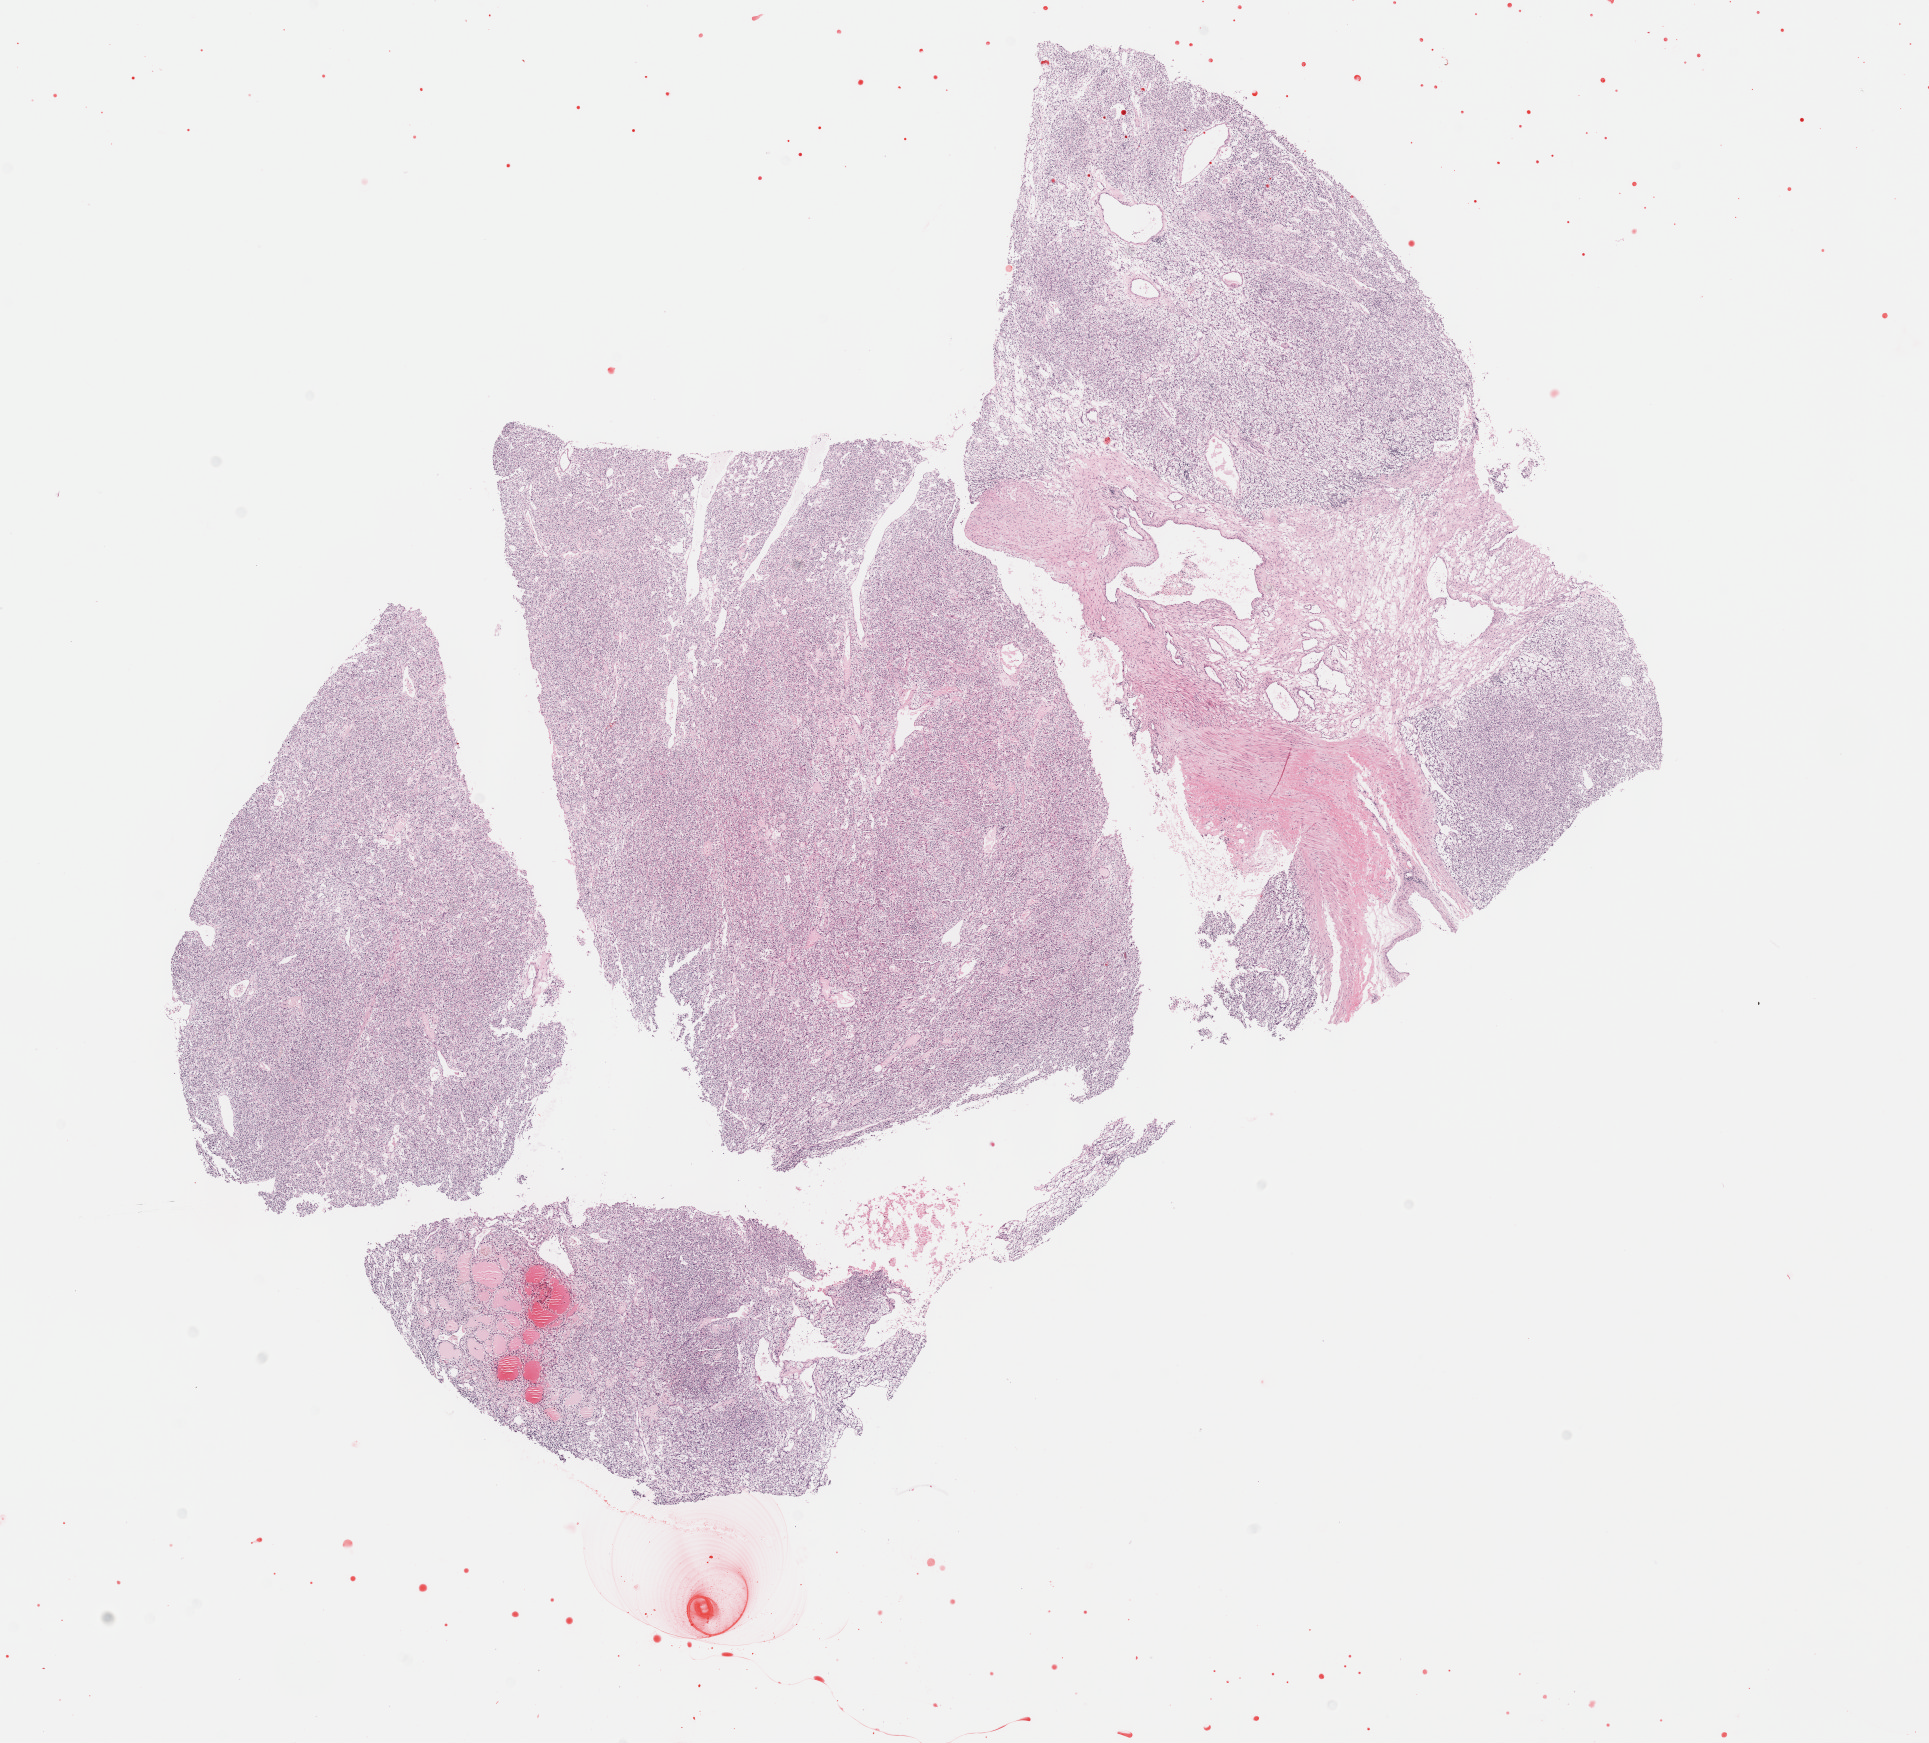
Digitized H&E tissue section (whole slide) — a low-resolution overview of the entire scanned area, about 15.6 x 14.1 mm (from a 40x scan); formalin-fixed paraffin-embedded (FFPE) diagnostic section; sample: primary tumour, kidney. Female patient; age at initial diagnosis 80 years. Histologic grade: G2 (moderately differentiated).
AJCC pathologic stage: I. Histologic diagnosis: Clear cell adenocarcinoma, NOS.